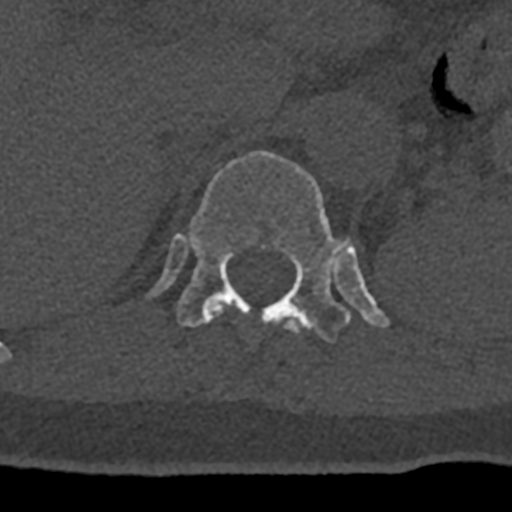
CT including the spine, one axial slice. Position 503 of 797 along the scan axis. Reconstruction kernel Br40s/3. 120 kVp. Bone window (W 1800 / L 400 HU). 512 × 512 image matrix, field of view 160 × 160 mm. Male patient, age 74 years. Case-level facts recorded for this patient, not image findings: primary cancer: renal.
Structures marked on this image (semi-automatic segmentation, software-assisted and operator-edited):
- T11 vertebra: bounding box (x1, y1, x2, y2) in pixels: (212, 305, 301, 333)
- T12 vertebra: (145, 151, 390, 343)